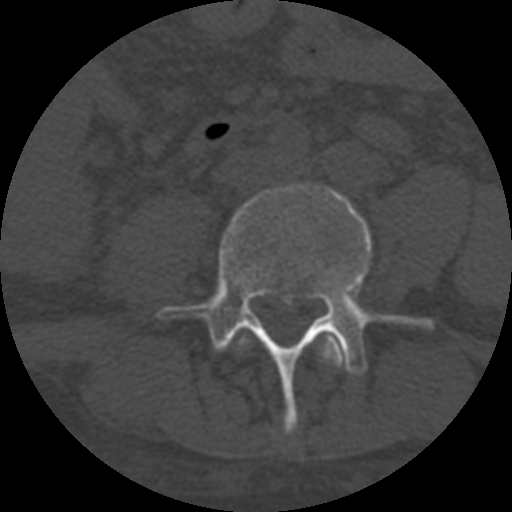
CT including the spine, one axial slice; reconstruction kernel STANDARD; 120 kVp; one of 3 acquisitions stored at this slice position; bone window (W 1800 / L 400 HU); 1.25 mm slice thickness; 512 × 512 image matrix, field of view 160 × 160 mm. Patient age 55 years. Case-level facts recorded for this patient, not image findings: primary cancer: colon; vertebrae with lytic lesions (as recorded): T12, L1, L5.
Outlined on this slice (semi-automatically segmented with operator editing):
- L3 vertebra: bounding box [x1, y1, x2, y2] px = [239, 336, 345, 367]
- L4 vertebra: [158, 183, 434, 432]